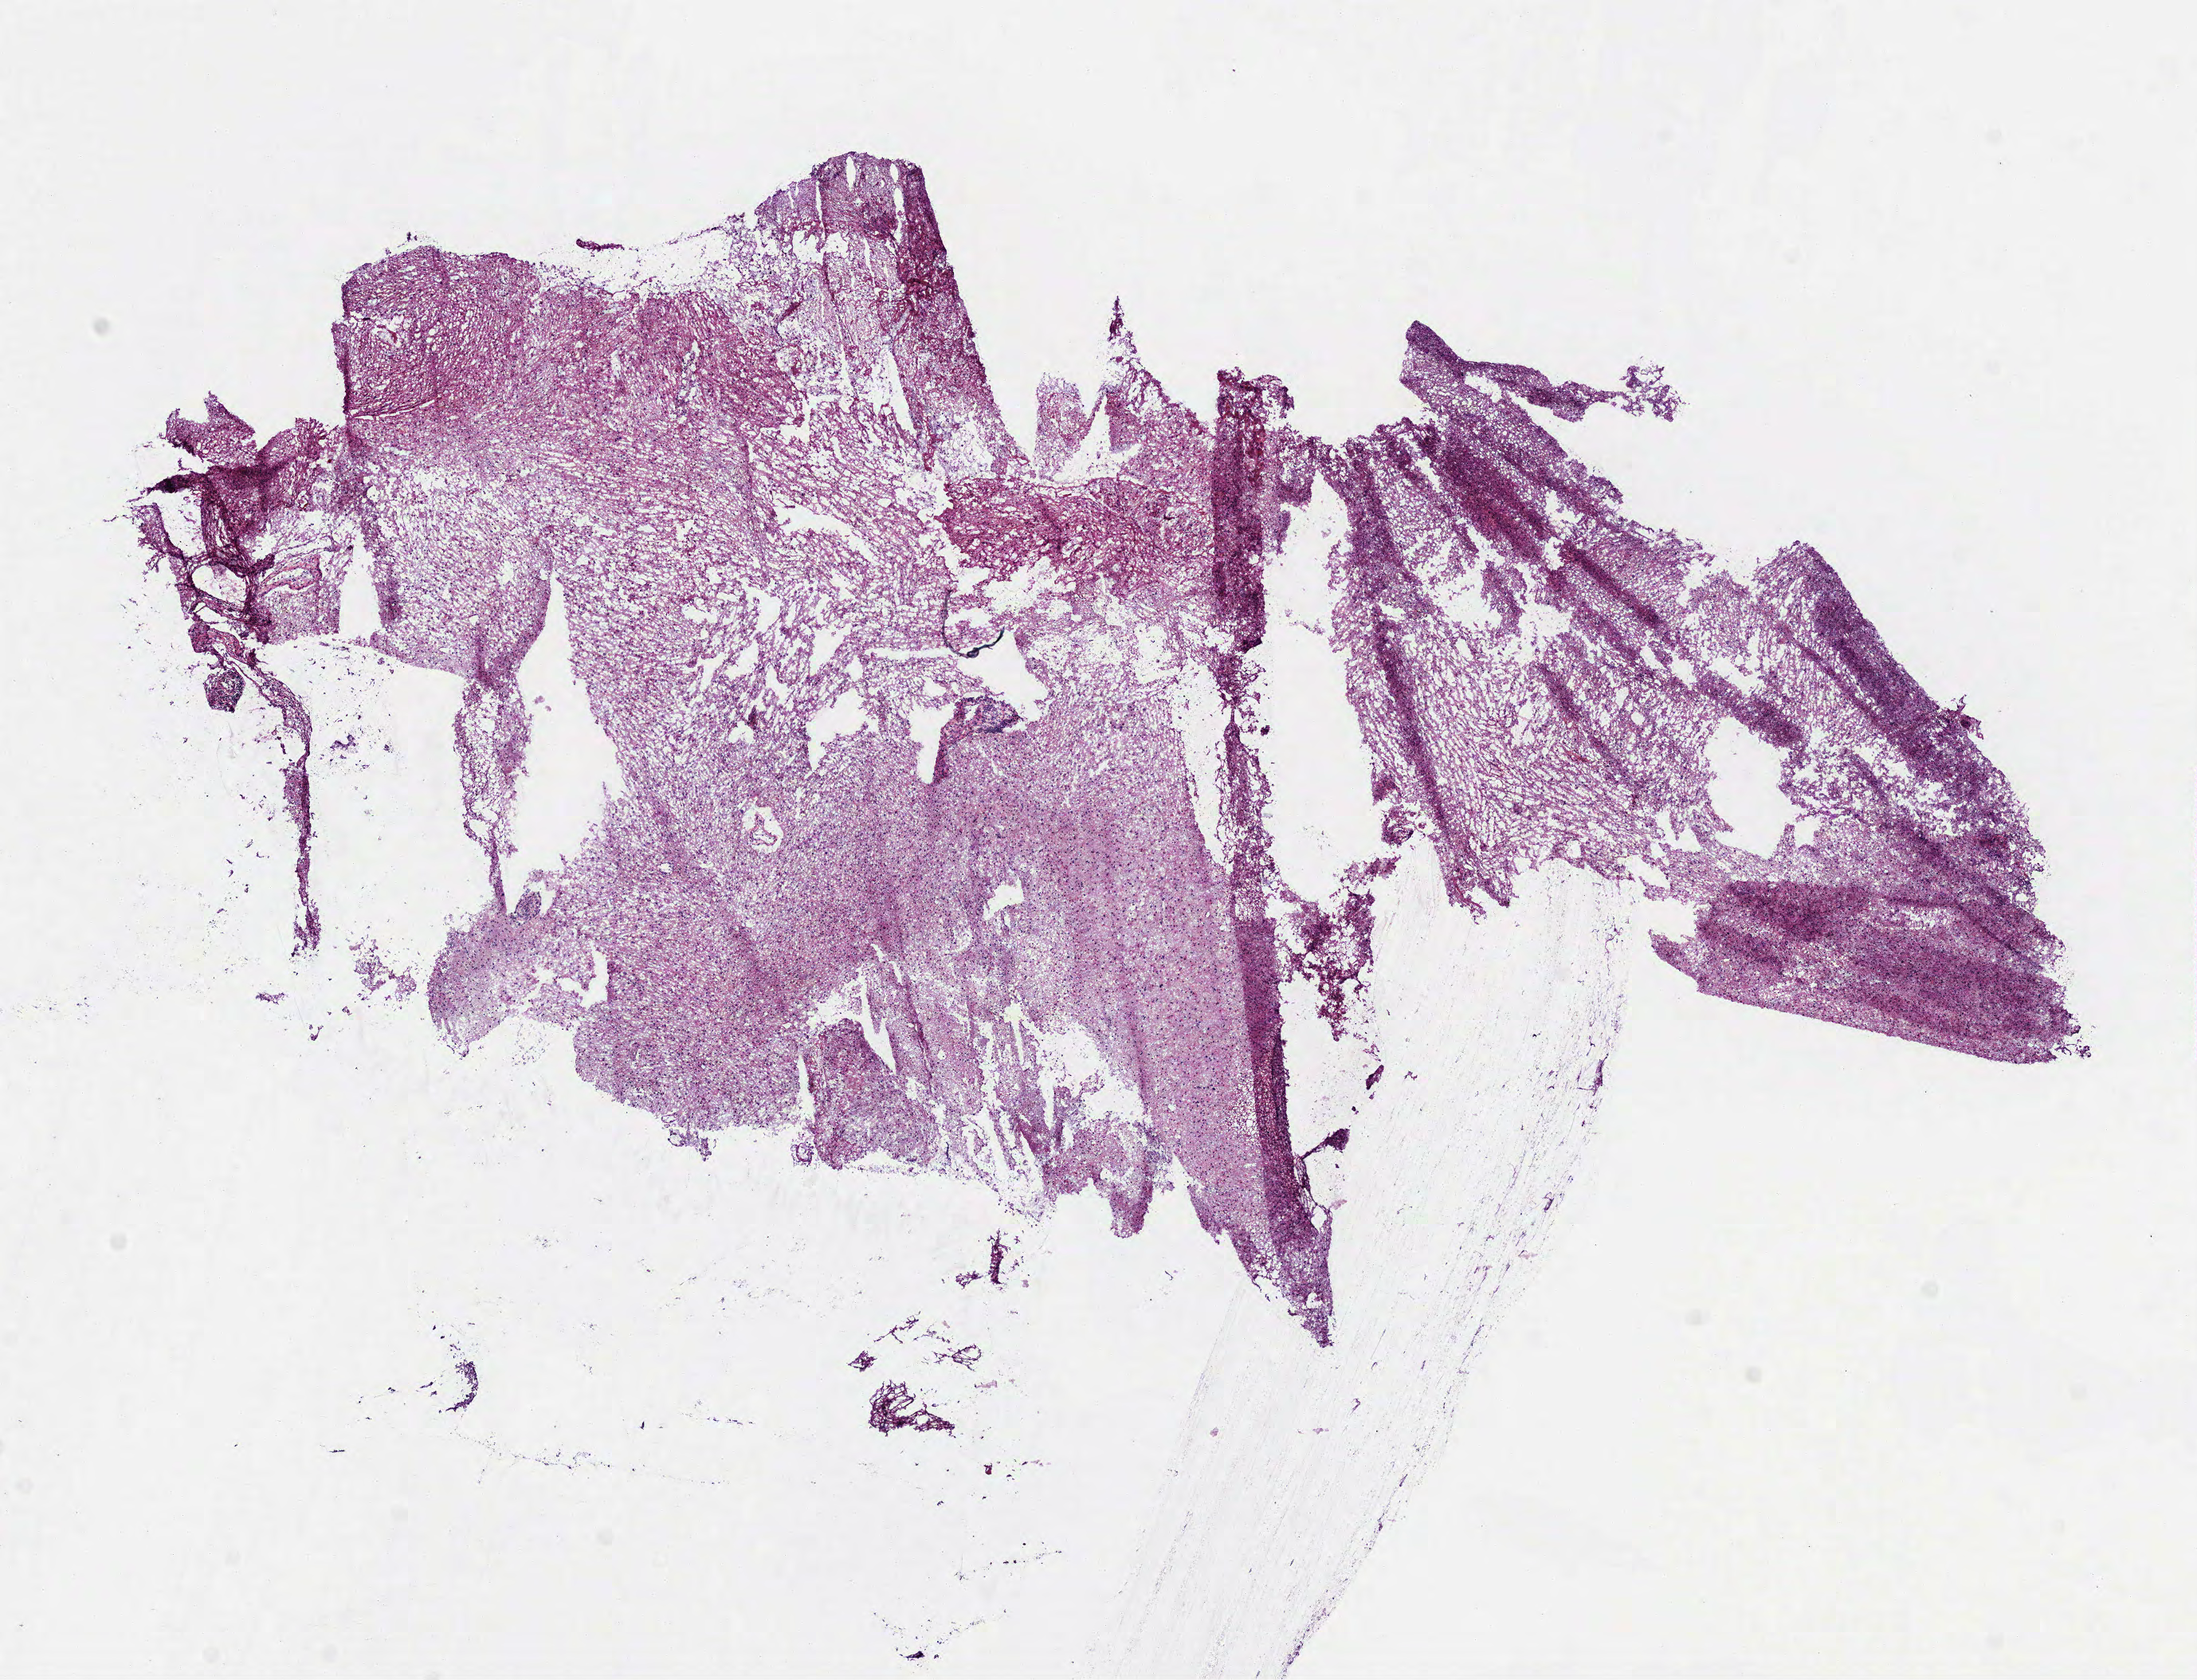
H&E whole-slide image, low-resolution overview of the scanned area, about 11.1 x 8.5 mm (slide scanned at 40x); frozen section; primary tumour sample from the brain. Male patient; age at initial diagnosis 28 years. Histologic grade: G2 (moderately differentiated). Slide review estimates, as recorded: tumour cells 100%, tumour nuclei 70%, normal cells 0%, stromal cells 0%, necrosis 0%.
Pathologic diagnosis: Astrocytoma, NOS (cerebrum).